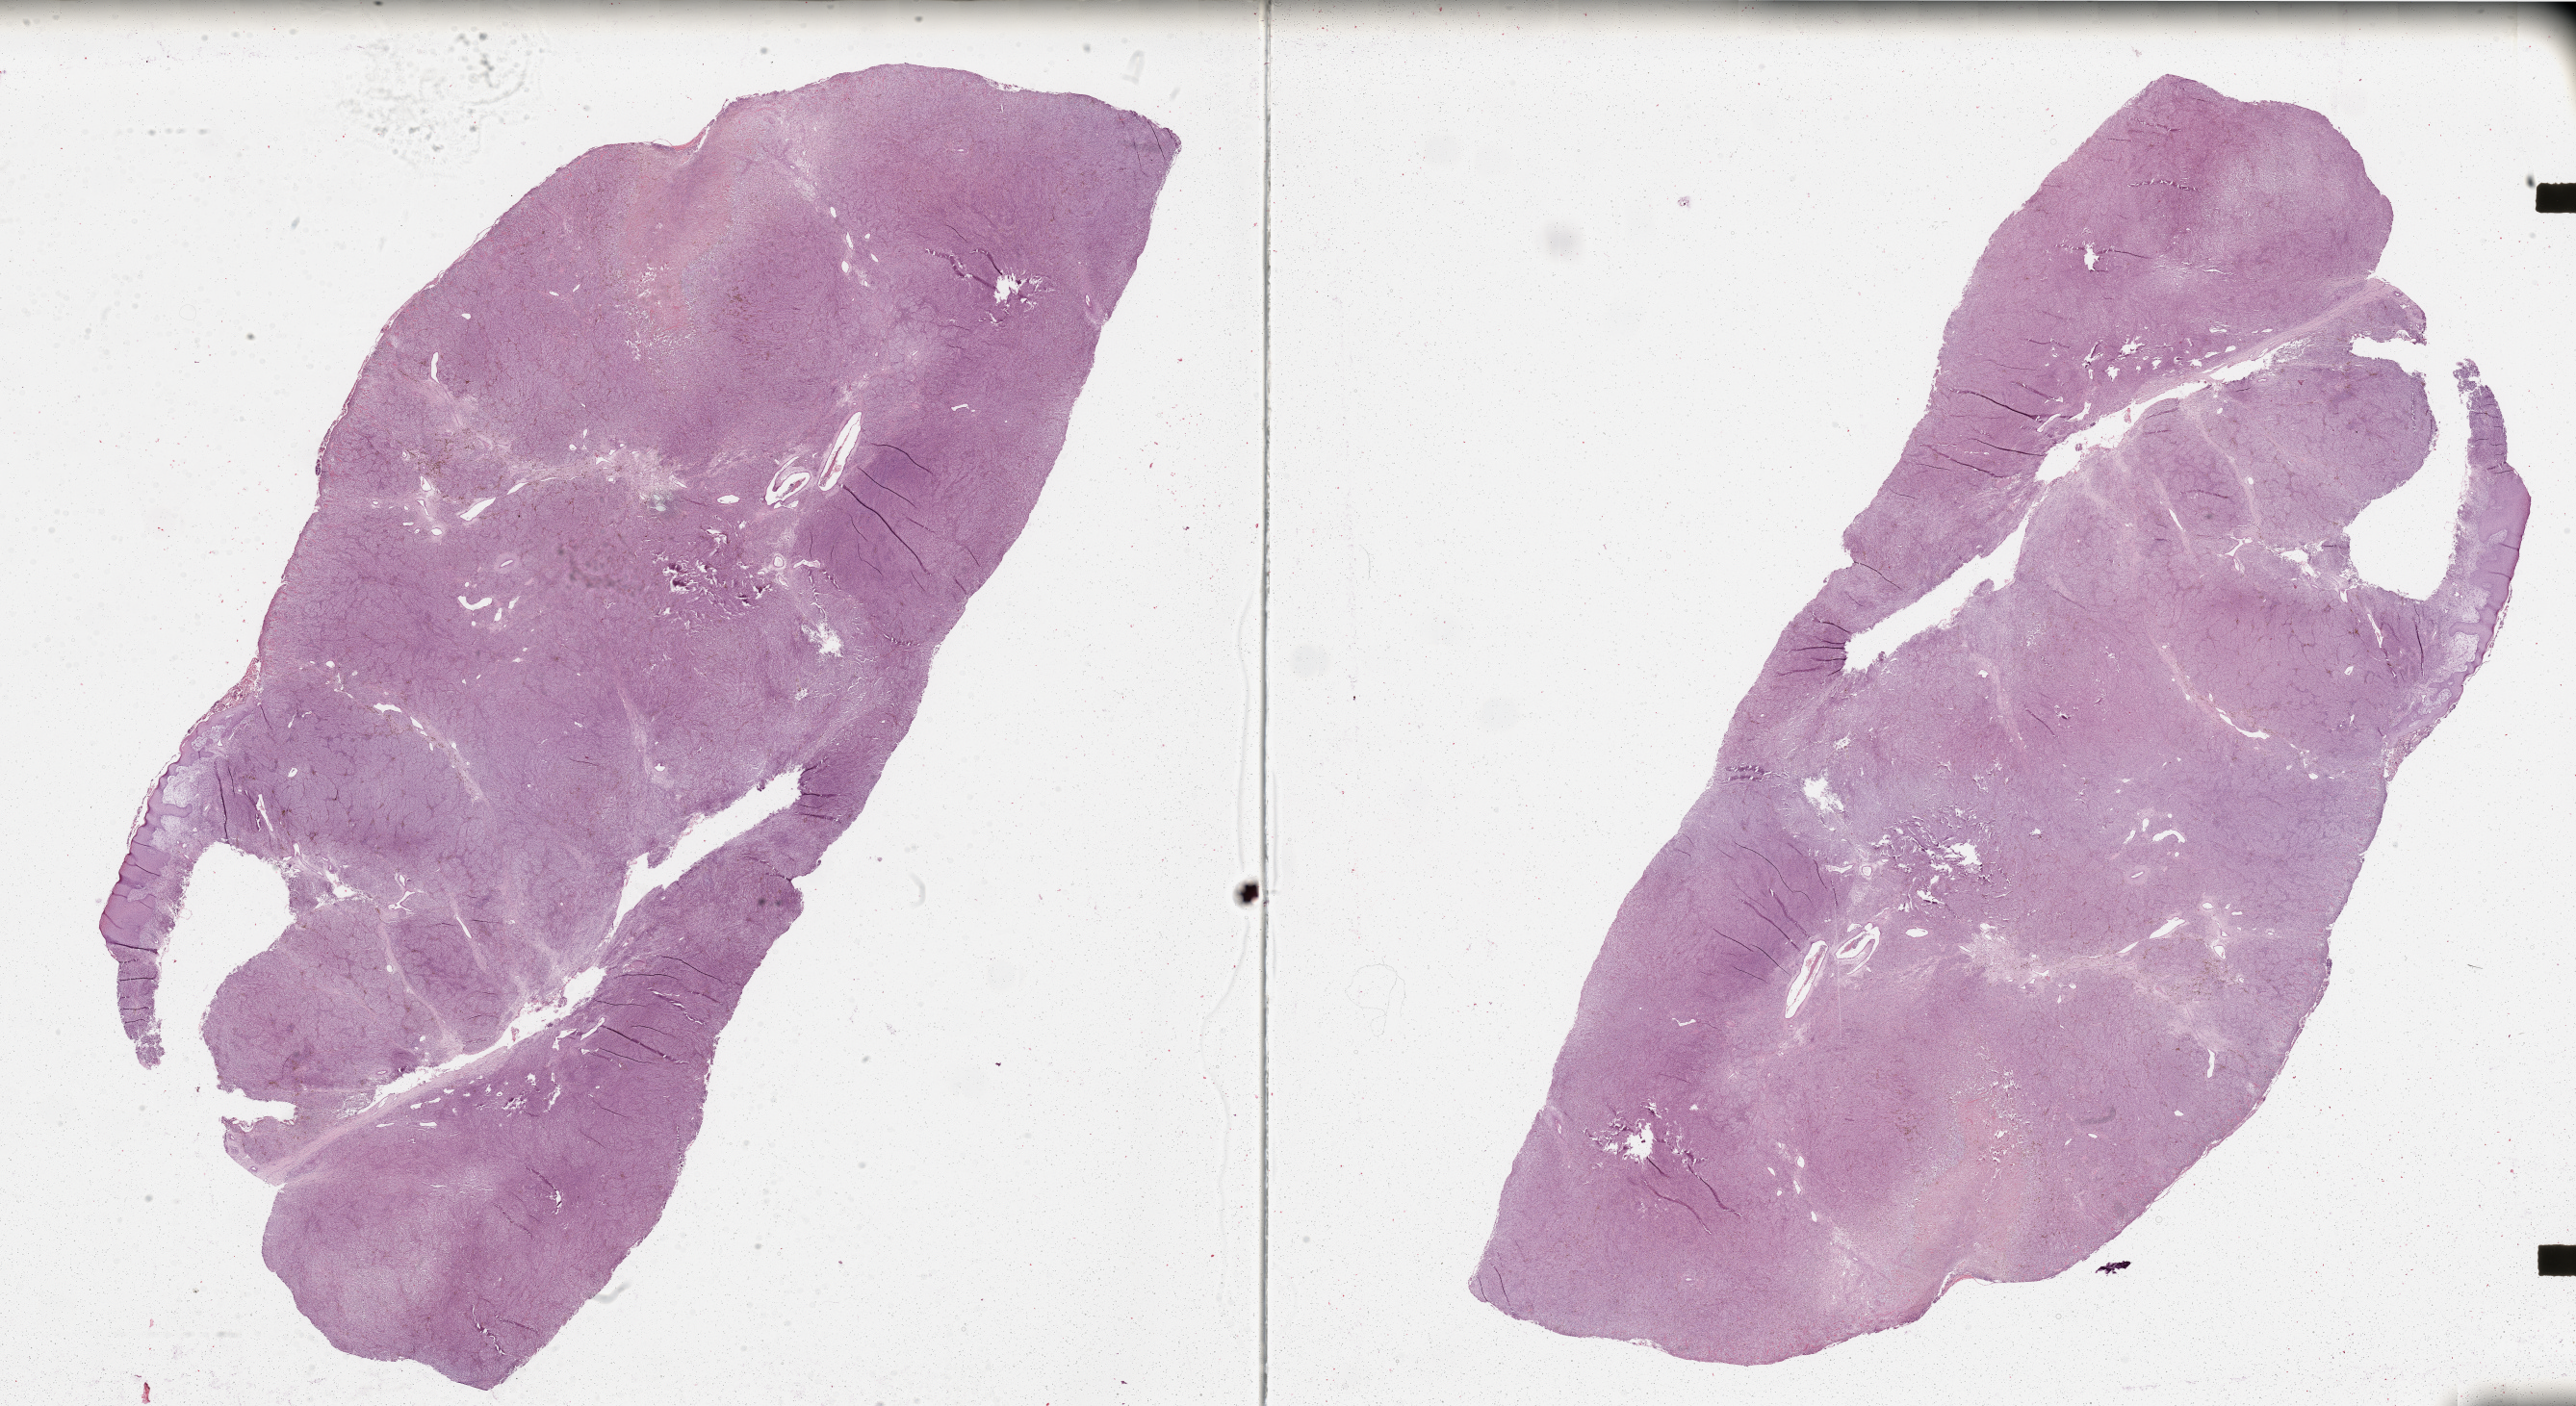
H&E-stained whole-slide image — whole scanned area (about 42.3 x 23.1 mm, slide scanned at 20x) shown as a low-resolution overview. Melanoma tumour tissue; sampled site not recorded. Male, 74 y/o.
AJCC pathologic stage: IIC. Histologic diagnosis: Malignant melanoma, NOS.